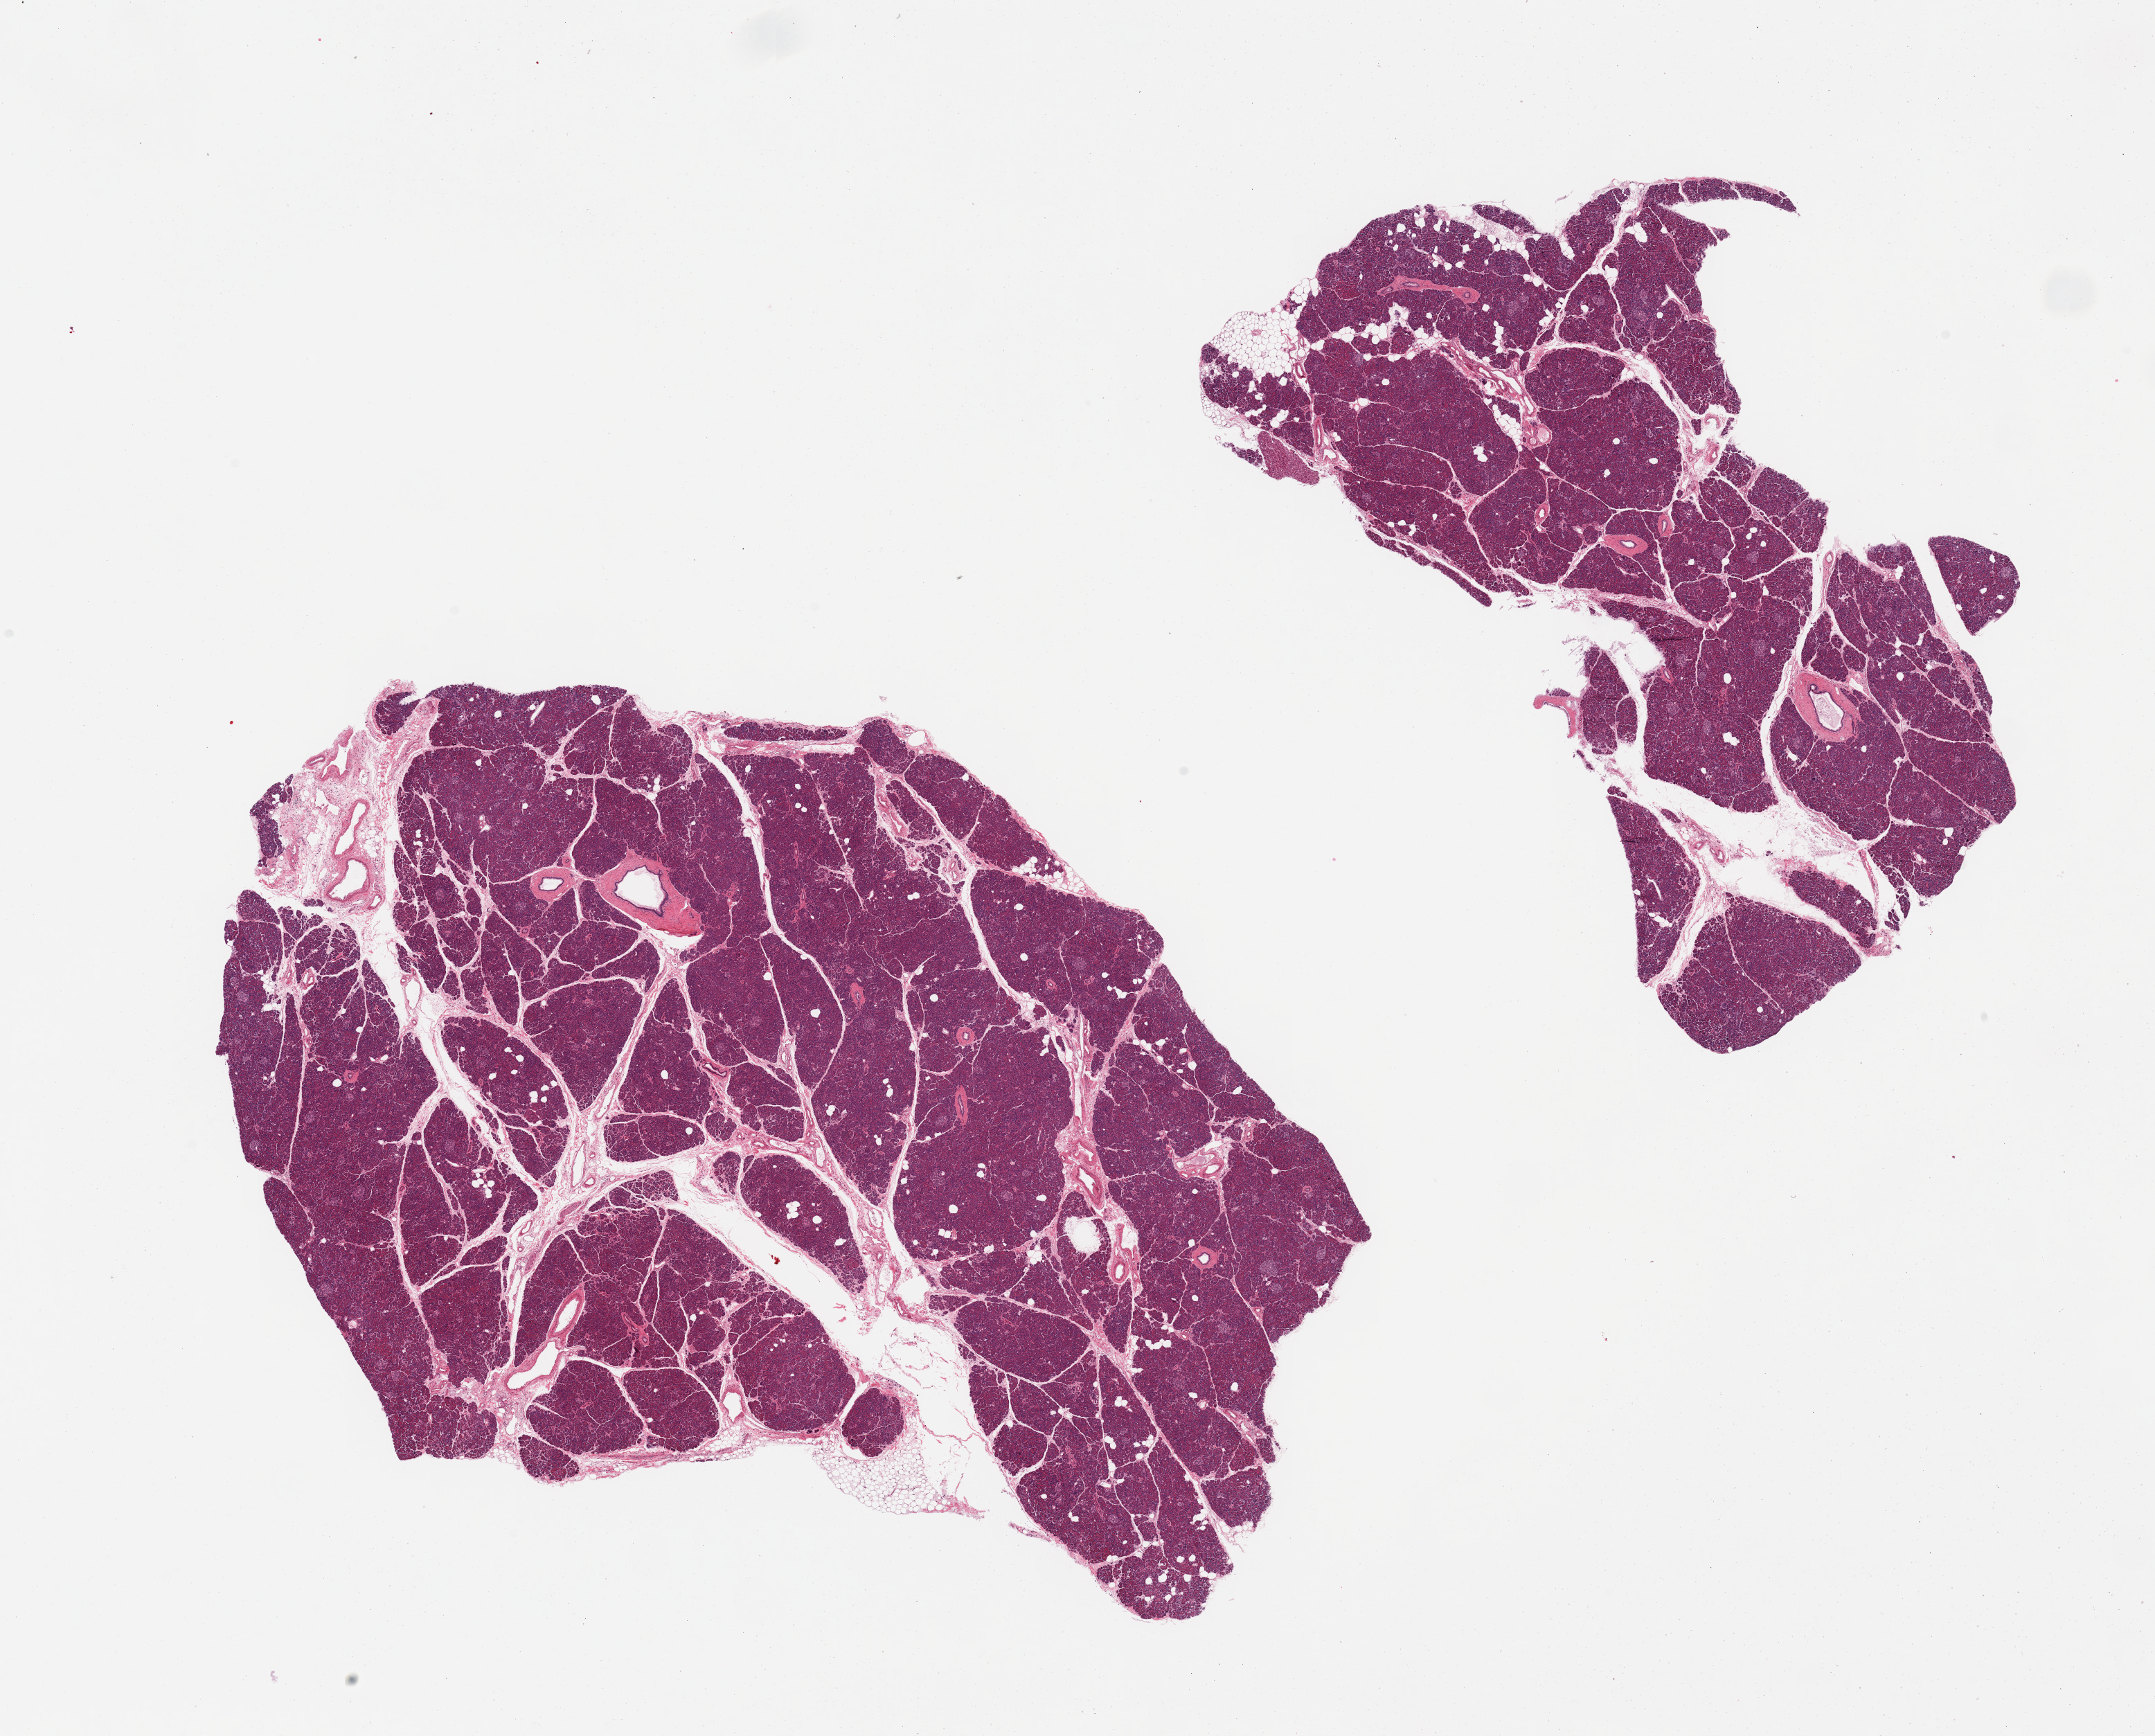
Haematoxylin and eosin whole-slide image, brightfield, low-resolution overview of the scanned area, about 24.6 x 19.8 mm. PAXgene-fixed paraffin-embedded (PFPE) section. Target tissue: pancreas. Tissue donor sample. Female donor.
Review note (as recorded): 2 pieces.